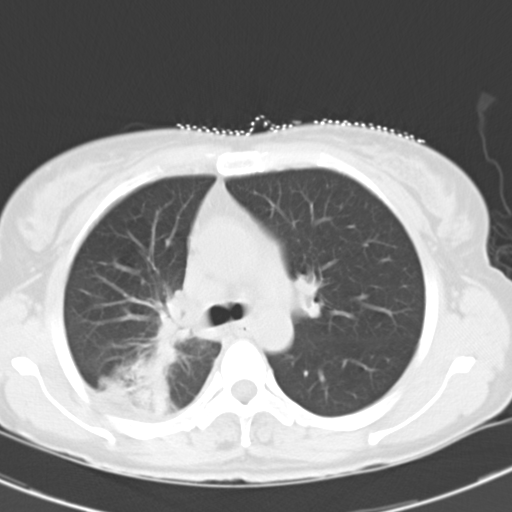
Chest CT, one axial slice; position 20 of 29 along the scan axis; 120 kVp; lung window (W 1500 / L -600 HU); 8 mm slice thickness; 512 × 512 image matrix, field of view 300 × 300 mm. Patient: female, 47 years. From the clinical record (not read from this slice): clinical TNM (as recorded): T1c N3 M0.
Structures marked on this image (bounding box drawn by a radiologist):
- lung tumour (recorded histology: adenocarcinoma): bounding box (x1, y1, x2, y2) in pixels: (97, 338, 174, 420)